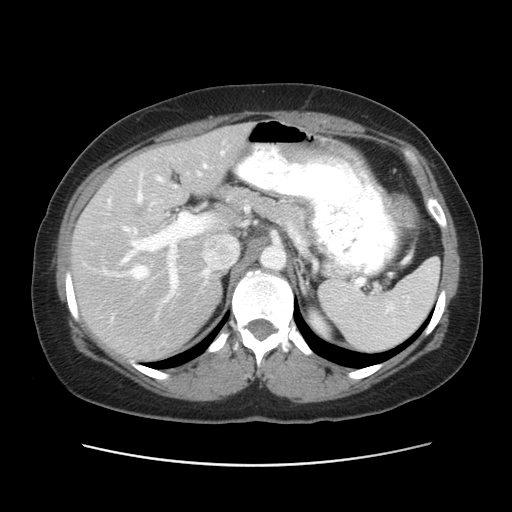
Contrast-enhanced abdominal CT, one axial slice; slice 34 of 52 in the series (ordered by position); soft-tissue window (W 400 / L 40 HU); 5 mm slice thickness; 512 × 512 image matrix. Female patient, age 48 years. Case-level facts recorded for this patient, not image findings: diagnosis: colorectal cancer liver metastases, imaged before liver resection; multiple liver metastases: yes; largest metastasis: 4.5 cm; disease in both lobes: yes.
Annotated regions visible in this slice (manually delineated by an expert):
- hepatic veins: box from (x=103, y=151) to (x=224, y=283) px
- liver: (x=71, y=127)–(x=247, y=357)
- planned liver remnant (the part of the liver to remain after resection): (x=153, y=127)–(x=248, y=199)
- portal vein (with intrahepatic branches): (x=98, y=164)–(x=210, y=304)
- liver metastasis: (x=128, y=202)–(x=152, y=221)